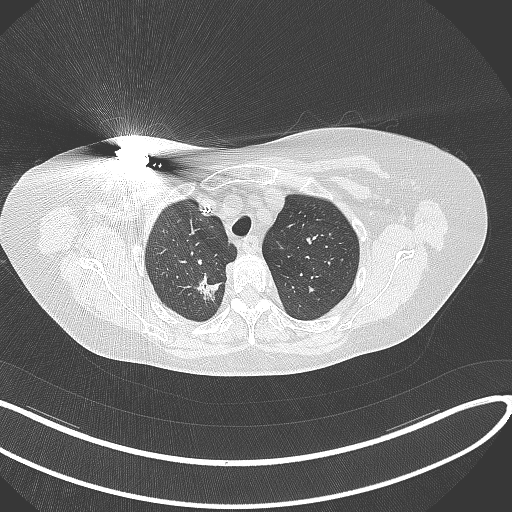
Chest CT, one axial slice; position 273 of 316 along the scan axis; 120 kVp; lung window (W 1500 / L -600 HU); 1 mm slice thickness; 512 × 512 image matrix. Female patient, age 72 years. Case-level facts recorded for this patient, not image findings: clinical TNM (as recorded): T1c N0 M0.
Annotated regions visible in this slice (rectangle marked by the reading radiologist):
- lung tumour (recorded histology: adenocarcinoma): box from (x=190, y=274) to (x=222, y=303) px